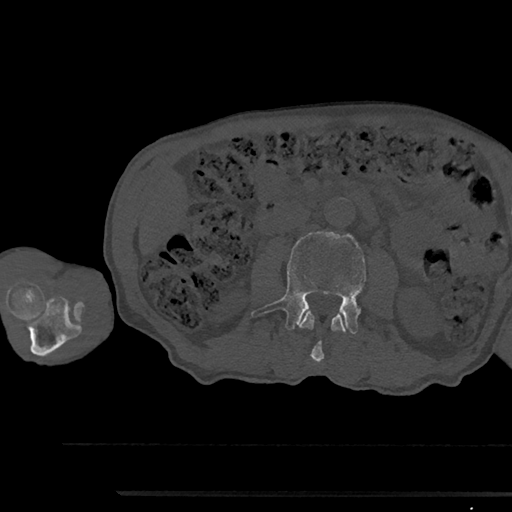
CT including the spine, one axial slice; 120 kVp; bone window (W 1800 / L 400 HU); 0.5 mm slice thickness; 512 × 512 image matrix, field of view 367 × 367 mm. Patient: male, 79 years. Case-level facts recorded for this patient, not image findings: primary cancer: prostate.
Outlined on this slice (semi-automatically segmented with operator editing):
- L2 vertebra: bounding box (x1, y1, x2, y2) in pixels: (298, 310, 347, 363)
- L3 vertebra: (251, 231, 366, 334)